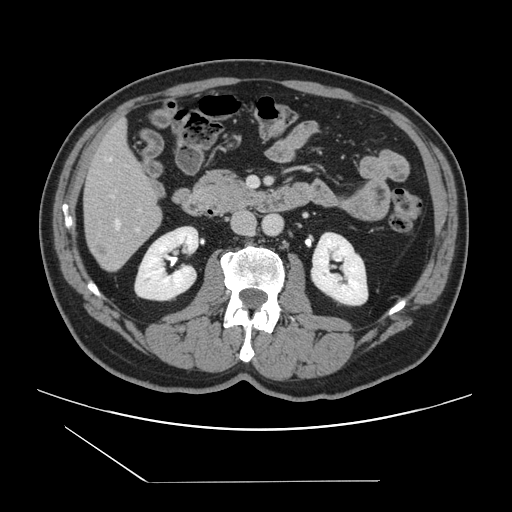
Contrast-enhanced abdominal CT, one axial slice; 120 kVp; intravenous contrast given; soft-tissue window (W 400 / L 40 HU); 512 × 512 image matrix, field of view 407 × 407 mm. Male patient, age 61 years. From the clinical record (not read from this slice): diagnosis: colorectal cancer liver metastases, imaged before liver resection; multiple liver metastases: yes; largest metastasis: 5.5 cm.
Structures marked on this image (manually delineated by an expert):
- hepatic veins: box from (x=108, y=158) to (x=120, y=229) px
- liver: (x=84, y=124)–(x=161, y=271)
- planned liver remnant (the part of the liver to remain after resection): (x=85, y=125)–(x=157, y=218)
- portal vein (with intrahepatic branches): (x=112, y=195)–(x=140, y=230)